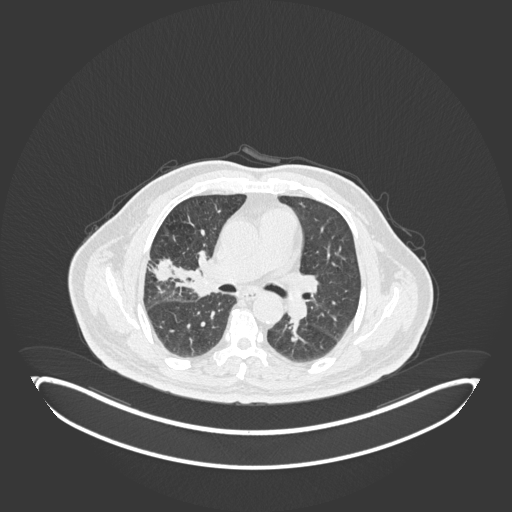
Chest CT, one axial slice; position 98 of 247 along the scan axis; reconstruction kernel B30f; 120 kVp; lung window (W 1500 / L -600 HU); 1 mm slice thickness; 512 × 512 image matrix, field of view 500 × 500 mm. Male patient, age 72 years. From the clinical record (not read from this slice): clinical TNM (as recorded): T1c N0 M0; histopathological grade: G2.
Structures marked on this image (rectangle marked by the reading radiologist):
- lung tumour (recorded histology: squamous cell carcinoma): box from (x=177, y=250) to (x=223, y=299) px